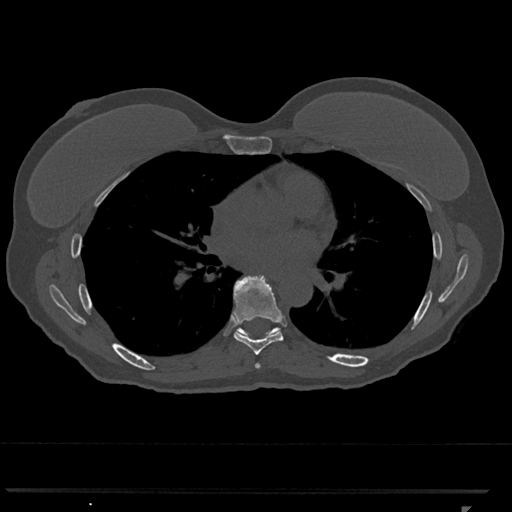
CT including the spine, one axial slice. Position 703 of 793 along the scan axis. Reconstruction kernel Br40s/3. 120 kVp. Bone window (W 1800 / L 400 HU). 512 × 512 image matrix, field of view 380 × 380 mm. Female patient, age 62 years. From the clinical record (not read from this slice): primary cancer: renal.
Structures marked on this image (semi-automatic segmentation, software-assisted and operator-edited):
- T6 vertebra: bounding box (x1, y1, x2, y2) in pixels: (255, 363, 261, 369)
- T7 vertebra: (232, 275, 284, 355)
- T8 vertebra: (238, 327, 278, 335)